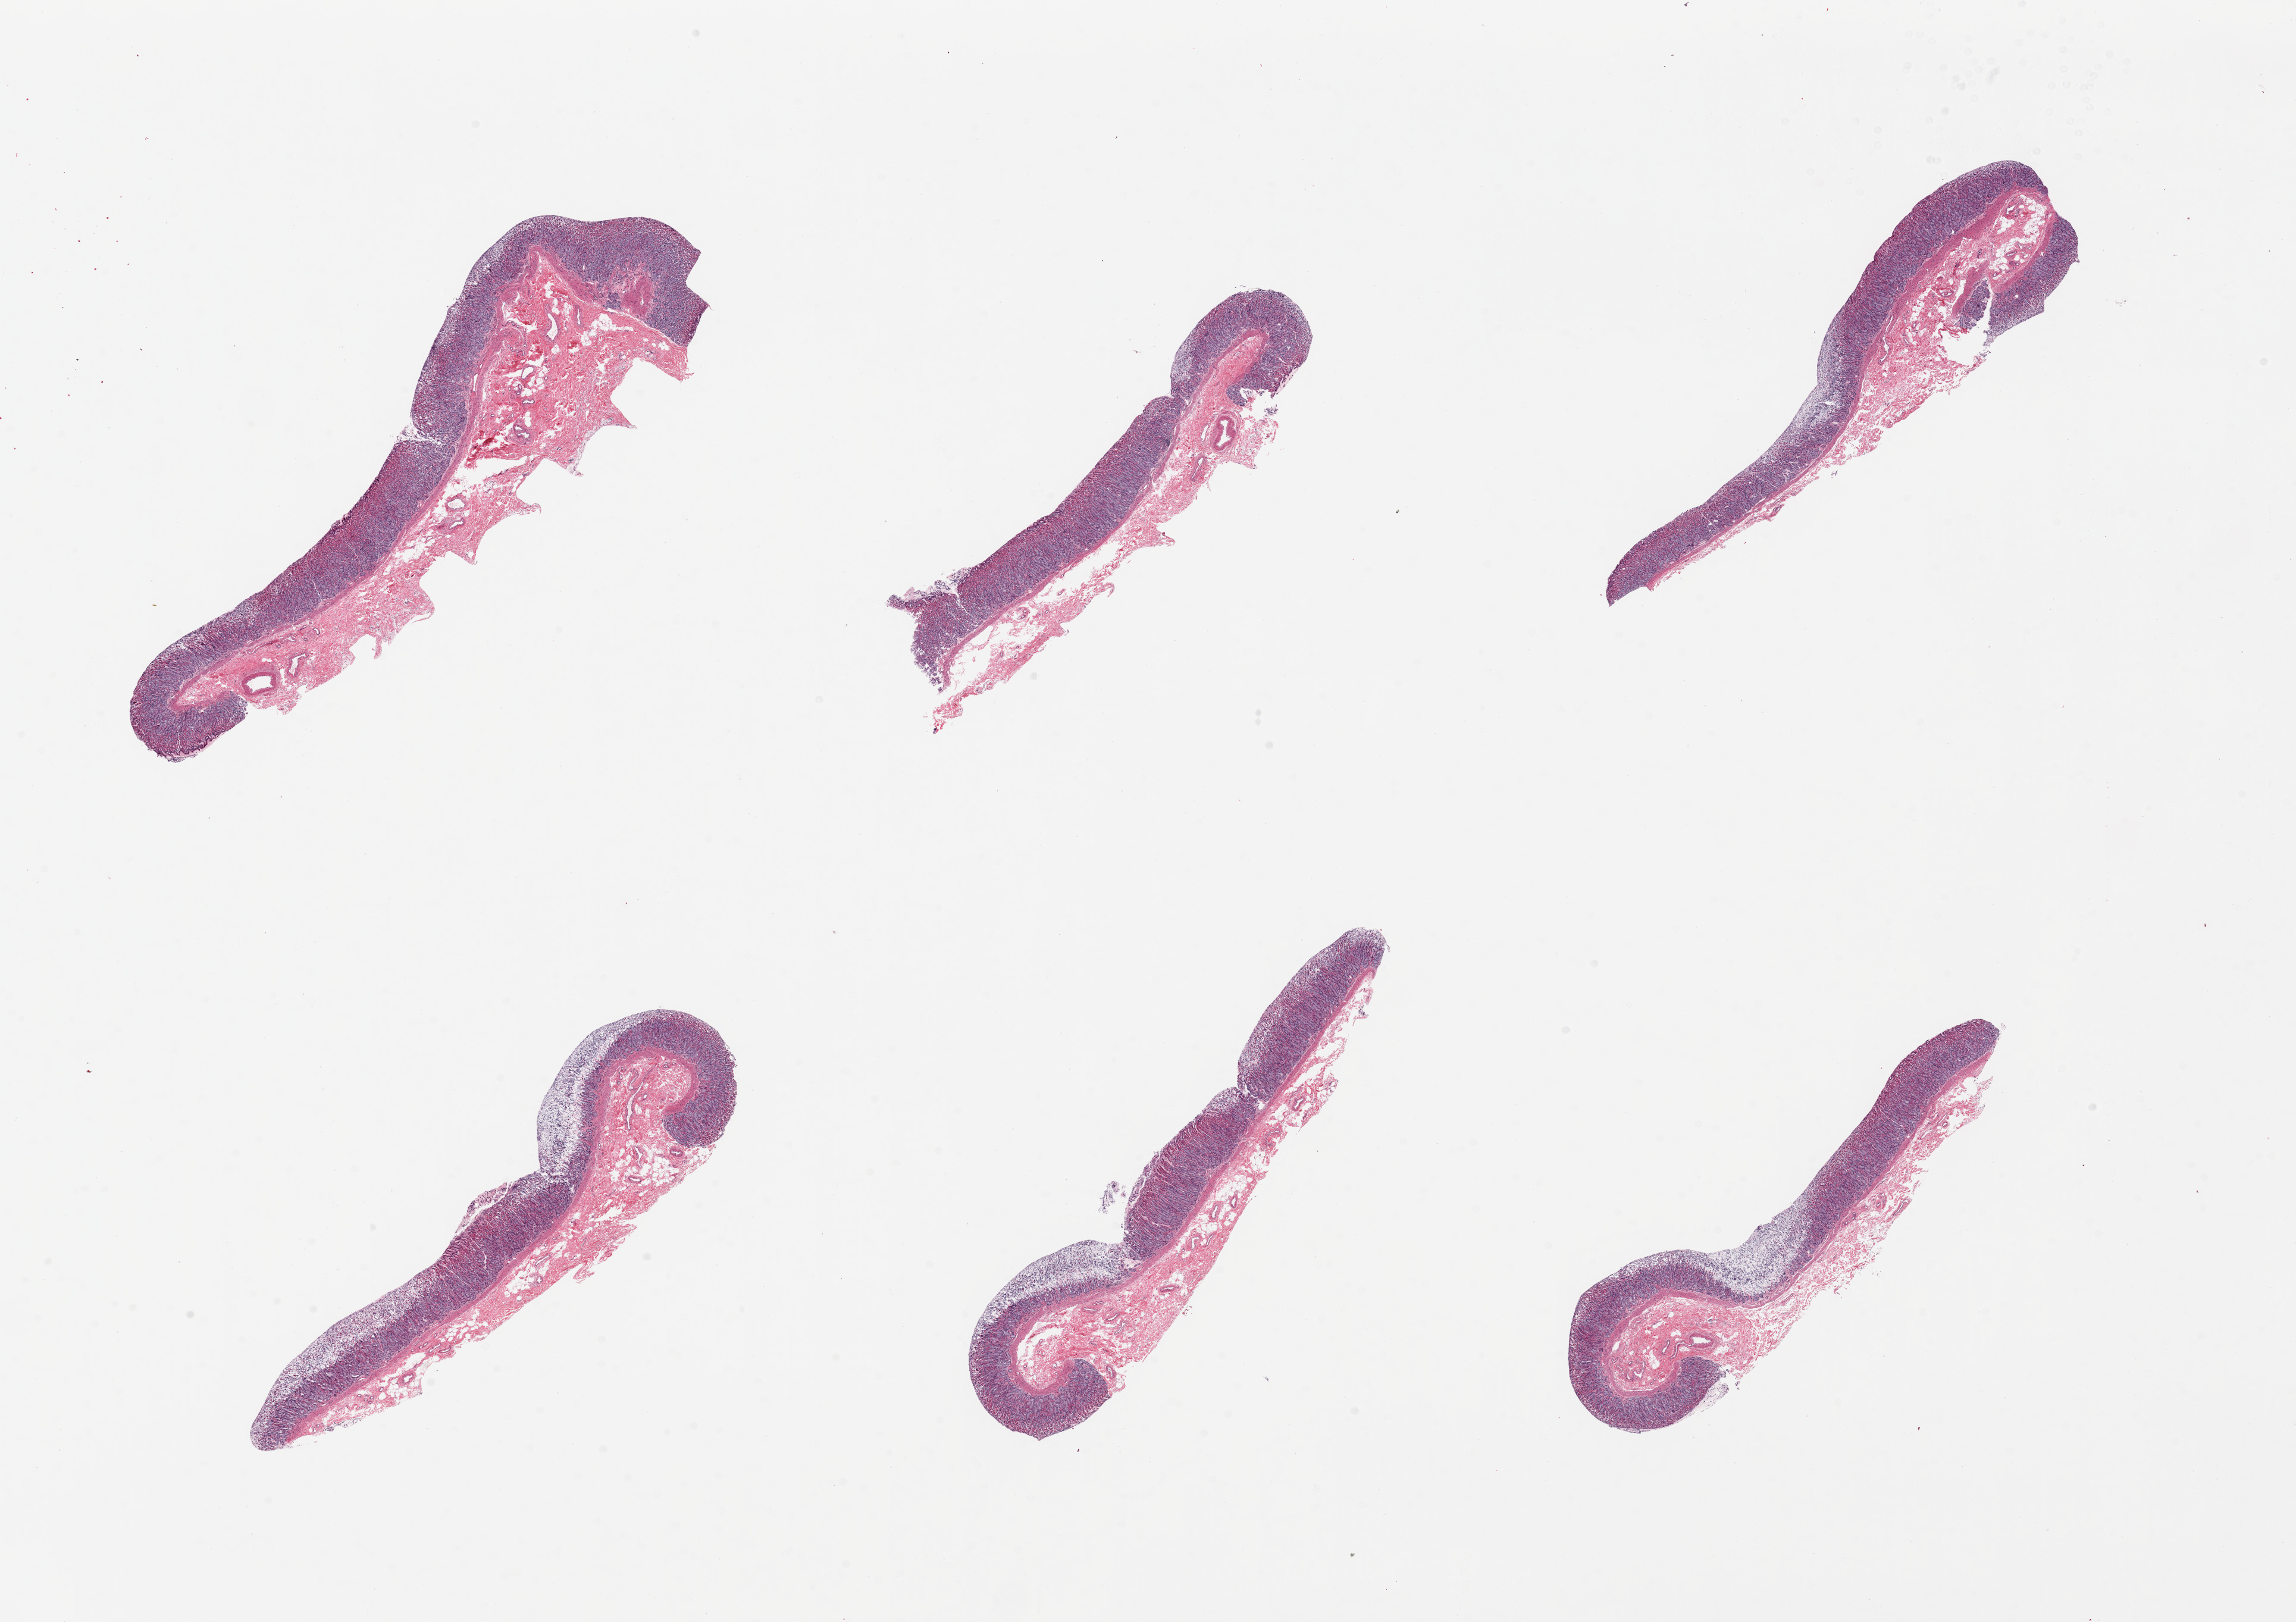
Whole-slide image, hematoxylin and eosin (H&E) stain, brightfield, low-resolution overview of the scanned area, about 30.5 x 21.6 mm, PAXgene-fixed paraffin-embedded (PFPE) section, target tissue: stomach, tissue donor sample. Donor: male.
Review note (as recorded): 6 pieces. Autolysis varies, focally severe. Mucosa only.